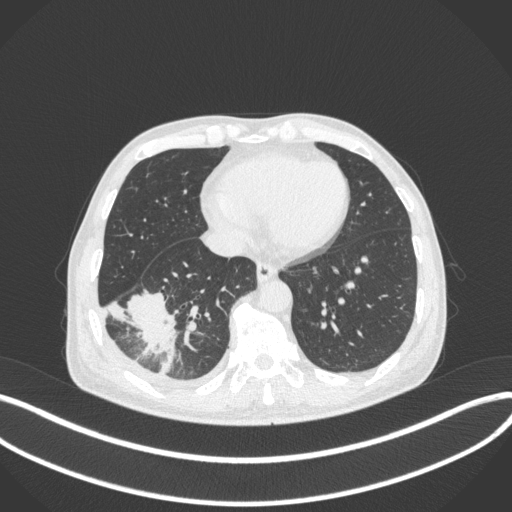
Chest CT, one axial slice. Lung window (W 1500 / L -600 HU). 1 mm slice thickness. 512 × 512 image matrix. Male patient, age 64 years. Case-level facts recorded for this patient, not image findings: clinical TNM (as recorded): T3 N0 M0.
Outlined on this slice (bounding box drawn by a radiologist):
- lung tumour (recorded histology: adenocarcinoma): bounding box <125,284,183,376> (left, top, right, bottom; pixels)